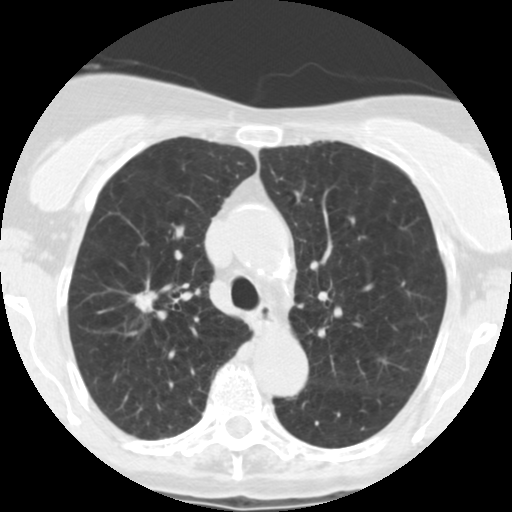
Low-dose screening chest CT, one axial slice. Slice 174 of 246 in the series (ordered by position). Reconstruction kernel STANDARD. Lung window (W 1500 / L -600 HU). 2.5 mm slice thickness. 512 × 512 image matrix.
Structures marked on this image (expert manual segmentation):
- lesion 1 (tumor, upper lobe of right lung): box from (x=130, y=285) to (x=158, y=313) px